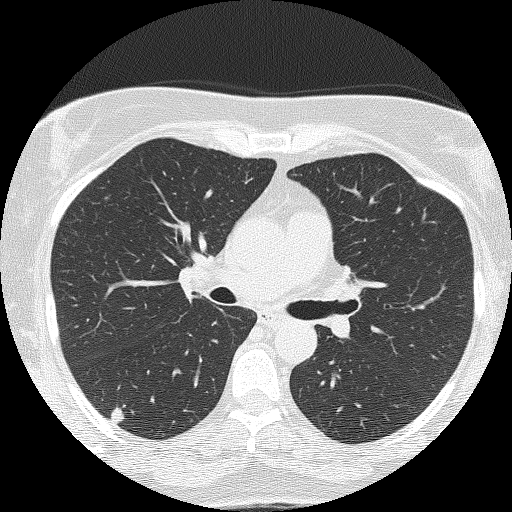
Low-dose screening chest CT, one axial slice. Position 84 of 143 along the scan axis. Reconstruction kernel FC51. 120 kVp. Lung window (W 1500 / L -600 HU). 2 mm slice thickness. 512 × 512 image matrix, field of view 301 × 301 mm.
Structures marked on this image (expert manual segmentation):
- lesion 1 (tumor, lower lobe of right lung): box from (x=111, y=408) to (x=125, y=423) px